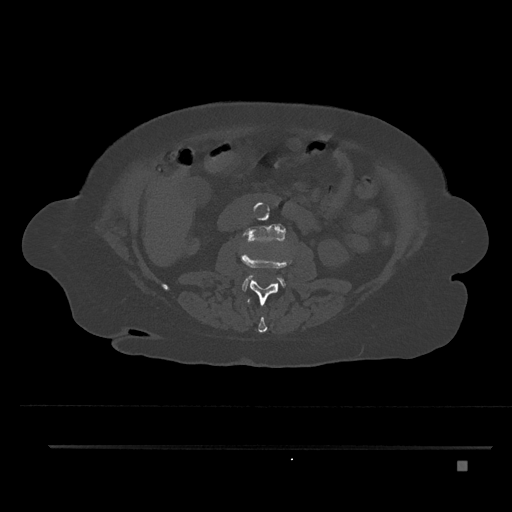
CT including the spine, one axial slice; slice 166 of 797 in the series (ordered by position); reconstruction kernel Br40s/3; 120 kVp; bone window (W 1800 / L 400 HU); 512 × 512 image matrix, field of view 437 × 437 mm. Patient: female, 76 years. From the clinical record (not read from this slice): primary cancer: lung.
Annotated regions visible in this slice (semi-automatic segmentation, software-assisted and operator-edited):
- L1 vertebra: bounding box [x1, y1, x2, y2] px = [247, 298, 267, 333]
- L2 vertebra: [241, 252, 292, 306]
- L3 vertebra: [242, 224, 286, 291]